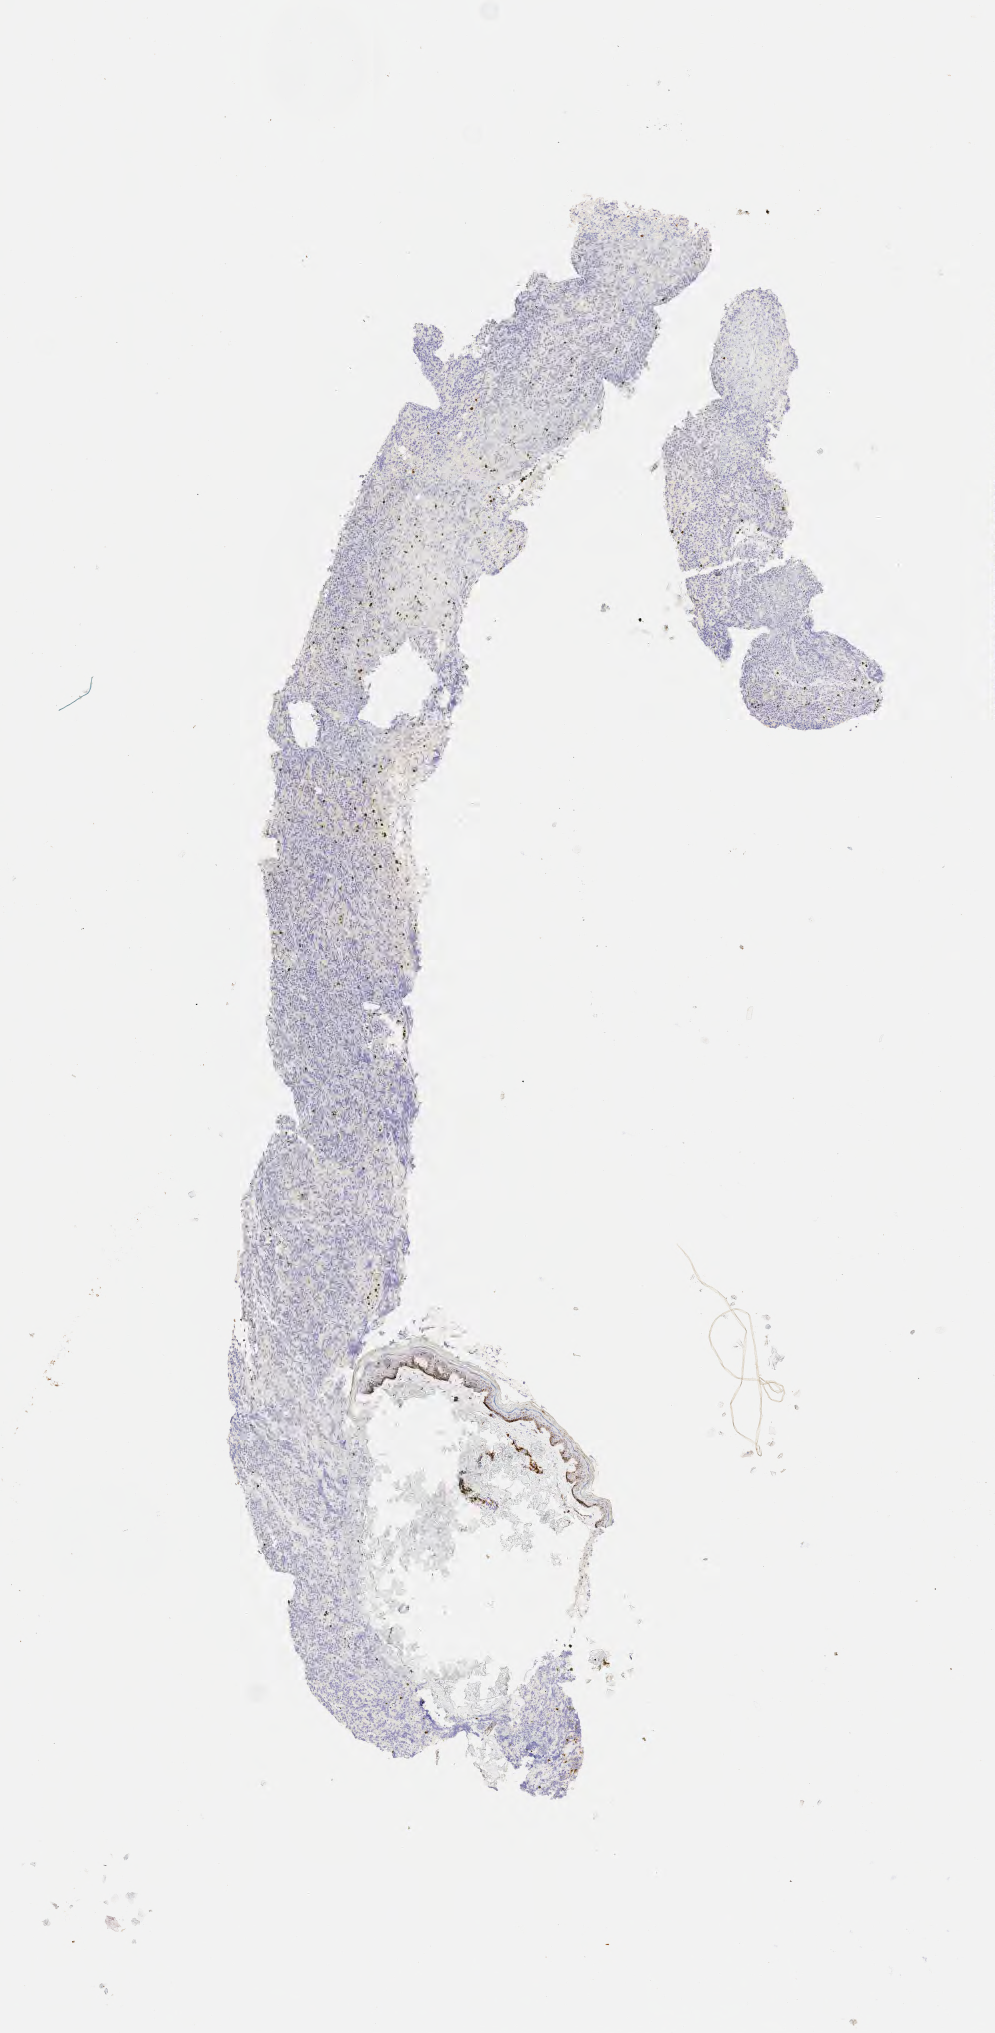
Immunohistochemistry (IHC) whole-slide image stained for CD3 — shown as a low-resolution overview of the whole scanned area (about 4.0 x 8.2 mm); tumor tissue. Female patient, aged 43.
- histologic diagnosis: Diffuse large B-cell lymphoma, NOS